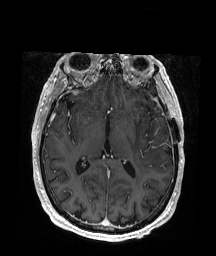
Brain MRI from a brain-tumour surgery series, one axial slice; slice 97 of 176 in the series (ordered by position); T1-weighted post-contrast; 216 × 256 image matrix, field of view 219 × 260 mm. From the clinical record (not read from this slice): histopathology: Glioblastoma; WHO grade: 4.
Annotated regions visible in this slice (outlined manually by an expert reader):
- tumour: bounding box (x1, y1, x2, y2) in pixels: (154, 131, 161, 136)